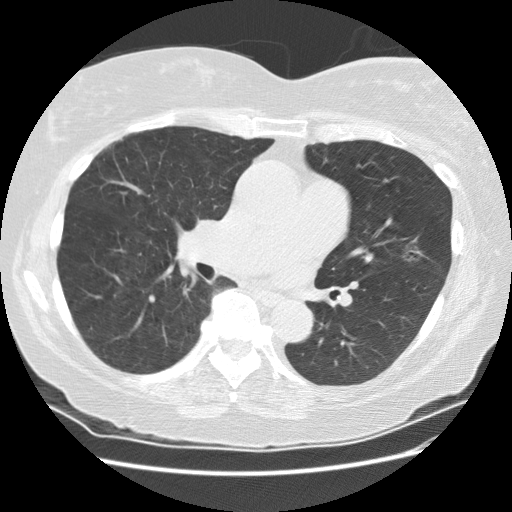
Chest CT (low-dose screening protocol), one axial image, second annual screen, lung window (W 1500 / L -600 HU), slice 98 of 180 in the series. Female participant, aged 71 years at enrolment.
Expert reader's lesion annotation, bounding box <387,226,439,269> (left, top, right, bottom; pixels). Screening reader's record for this exam (one nodule recorded; not confirmed to be the boxed lesion): non-calcified nodule or mass ≥4 mm, lingula, 13 × 13 mm, poorly defined margins, ground glass attenuation, pre-existing on the prior screen: yes; interval growth: yes. Lung cancer was diagnosed 26 days after this screen: adenocarcinoma, NOS, left upper lobe, well differentiated (G1), stage IA (AJCC 6th edition), 11 mm at pathology.